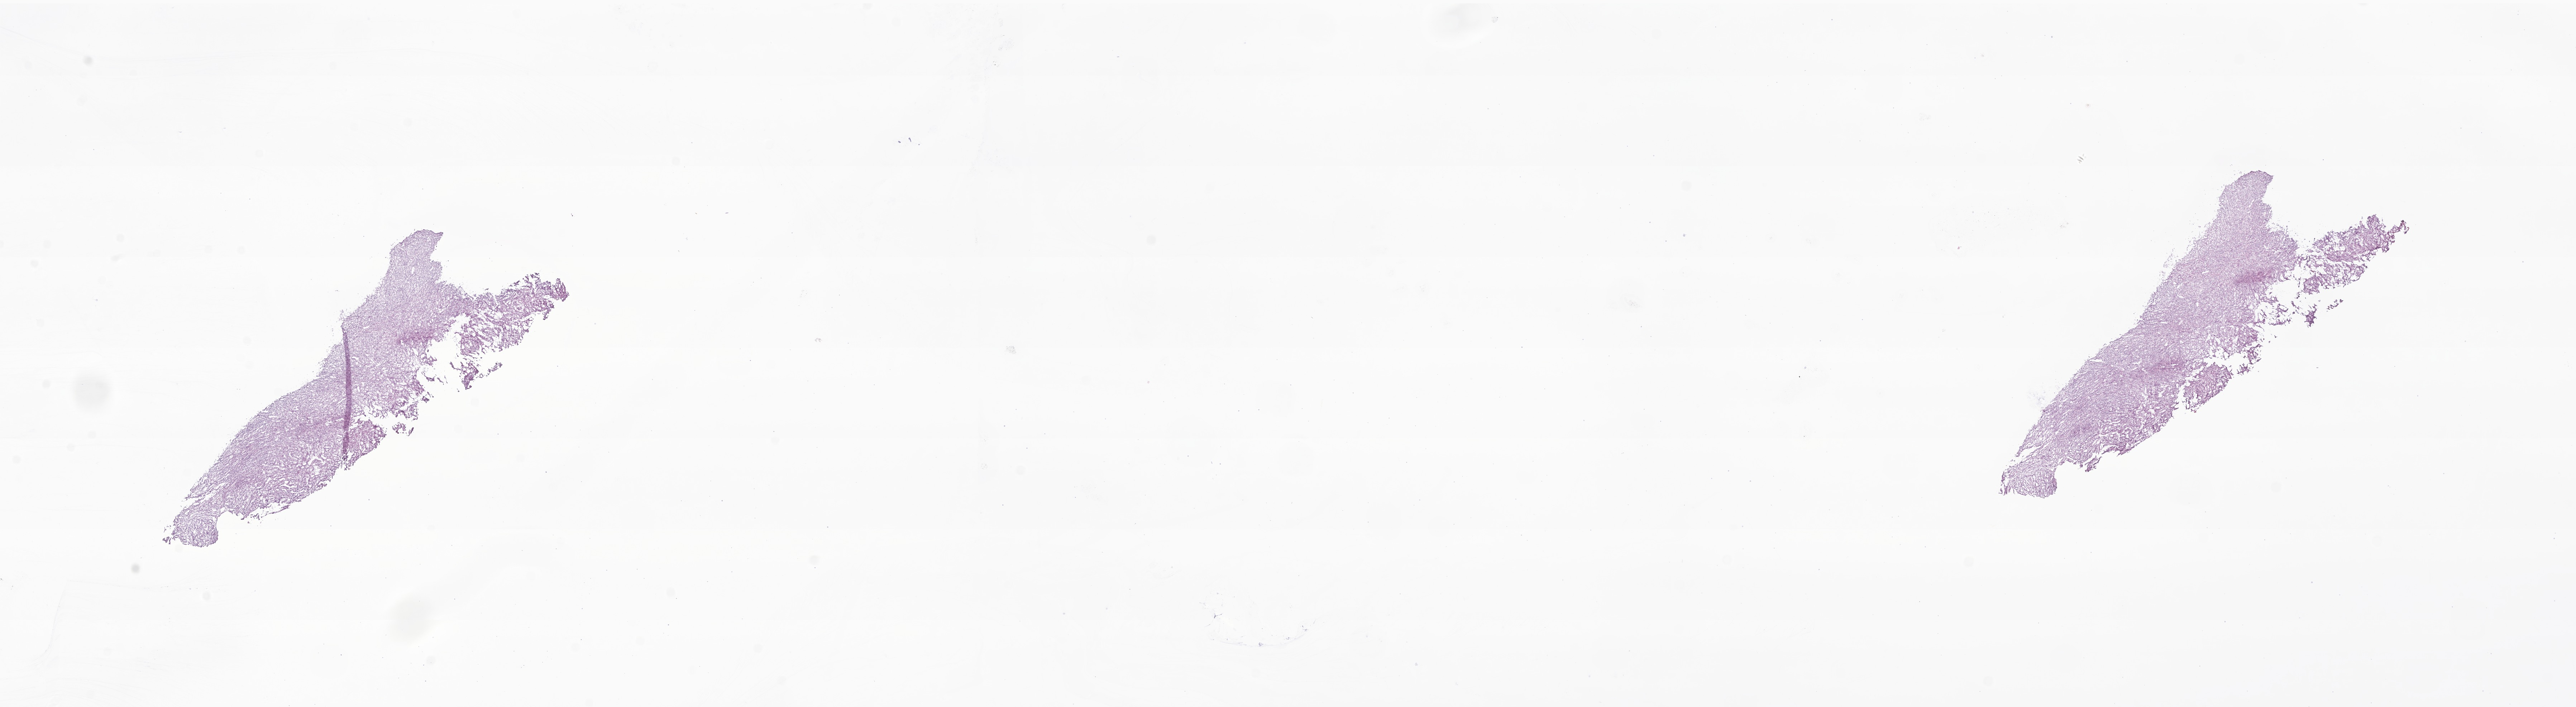
Digitized H&E-stained section of tumor tissue from the brain, a low-resolution overview of the entire scanned area, about 30.3 x 8.3 mm; frozen section (OCT-embedded). Patient female; age 649 days.
Diagnosis: Glioma, malignant.